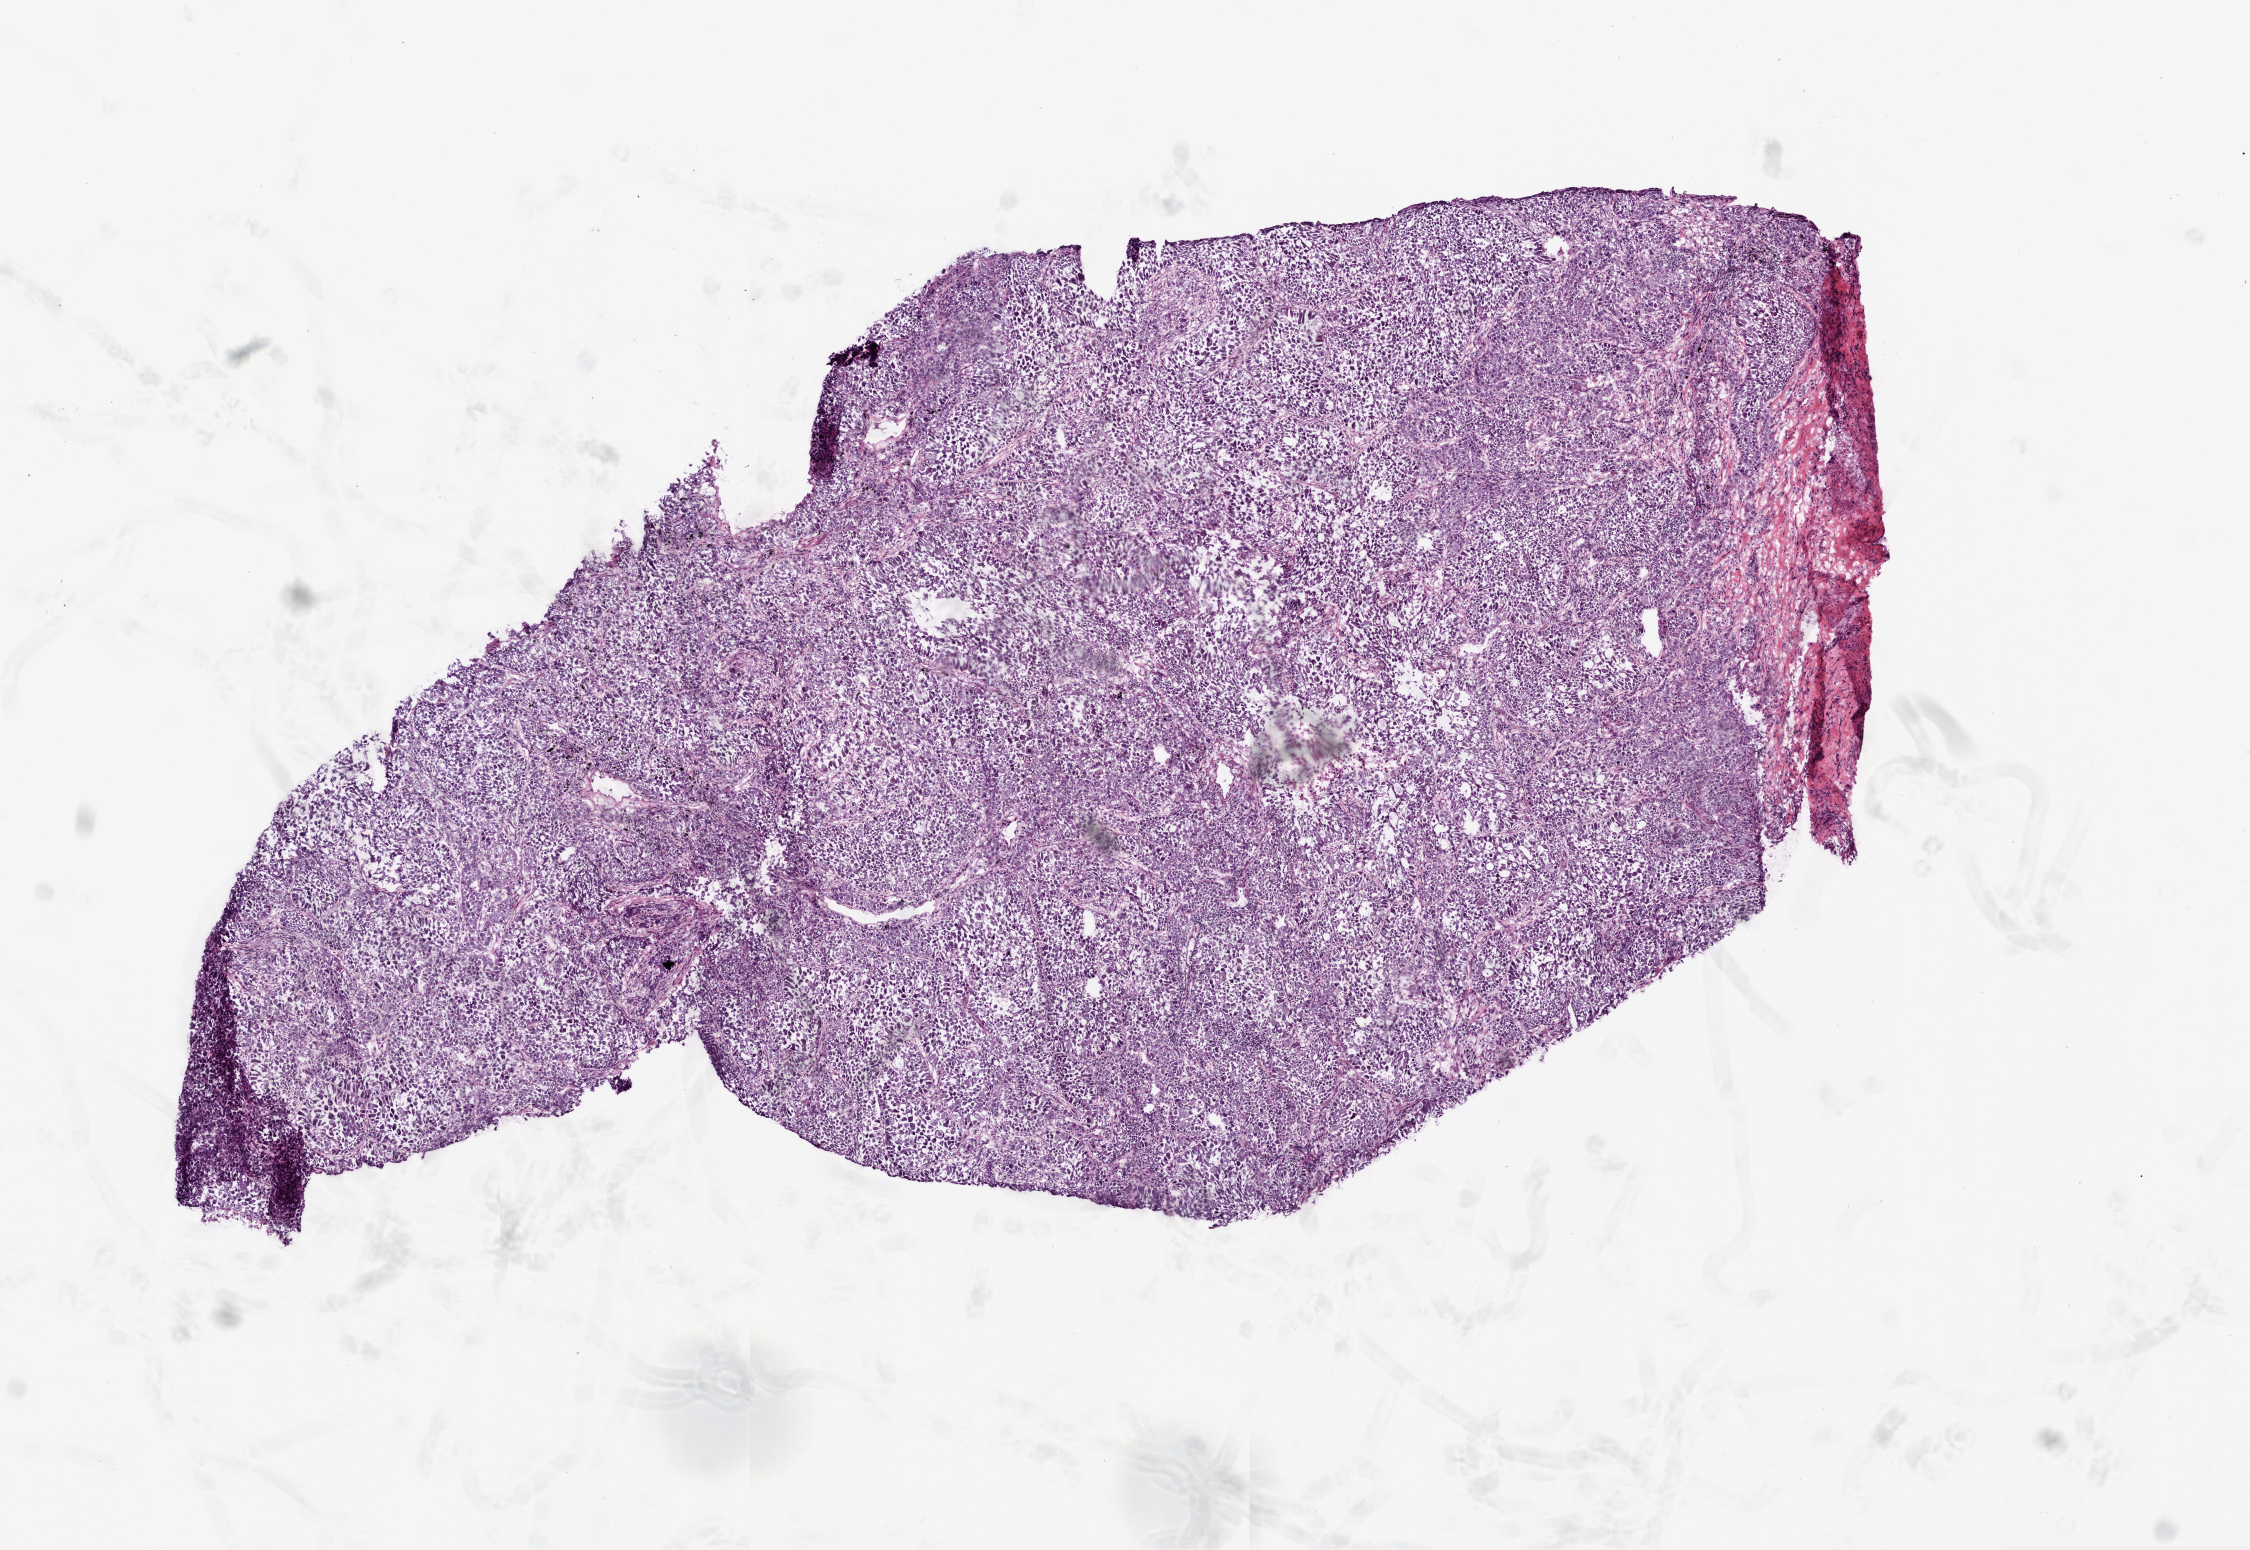
Whole-slide histology image, H&E-stained, a low-resolution overview of the entire scanned area, about 9.0 x 6.2 mm (from a 20x scan); frozen section; lung, primary tumour sample. Male patient; age at initial diagnosis 76 years. Composition of this section per pathologist review: tumour cells 95%, tumour nuclei 75%, normal cells 0%, stromal cells 5%, necrosis 0%.
- AJCC pathologic stage: IIIB (5th edition)
- diagnosis: Adenocarcinoma with mixed subtypes (upper lobe, lung)